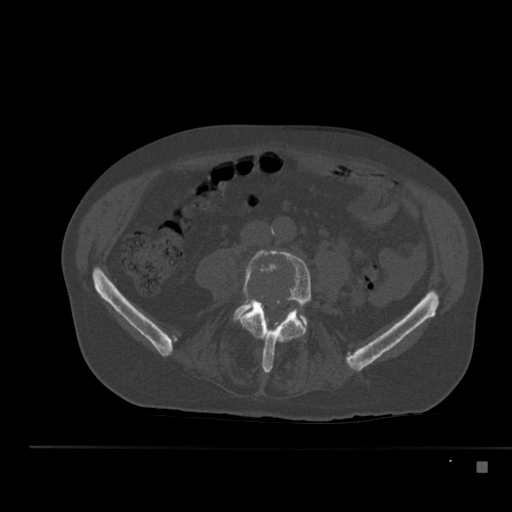
CT including the spine, one axial slice. Position 139 of 517 along the scan axis. Reconstruction kernel Br40s. 120 kVp. Bone window (W 1800 / L 400 HU). 1.5 mm slice thickness. 512 × 512 image matrix, field of view 408 × 408 mm. Patient: male, 70 years. Case-level facts recorded for this patient, not image findings: primary cancer: renal; vertebrae with lytic lesions (as recorded): T4, T6, T10, T12, L3, L4, L5.
Structures marked on this image (semi-automatically segmented with operator editing):
- L4 vertebra: bounding box <240,249,311,373> (left, top, right, bottom; pixels)
- L5 vertebra: <235,302,307,324>